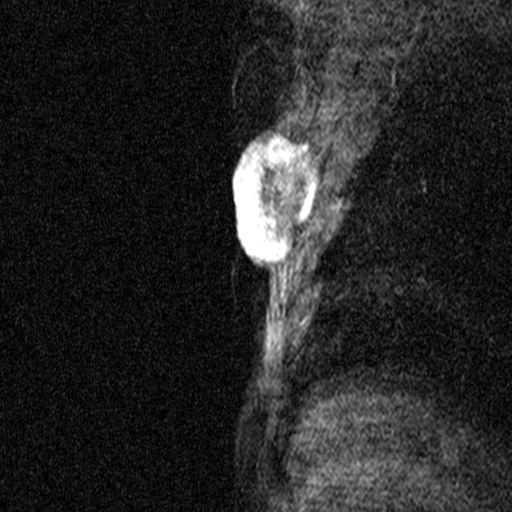
Breast MRI (dynamic contrast-enhanced), one sagittal slice. Slice 31 of 44 in the series (ordered by position). Dynamic contrast-enhanced study with each time point stored as its own series, time point 2 of 3 at this slice position (early post-contrast, ordered by acquisition time). 1.5 T. TE 4.5 ms, TR 11 ms. 3 mm slice thickness. 512 × 512 image matrix, field of view 200 × 200 mm. Female patient, age 44 years. From the clinical record (not read from this slice): setting: breast cancer imaged before/during neoadjuvant chemotherapy; receptor status: HR-positive, HER2-negative.
Annotated regions visible in this slice (semi-automatic segmentation, software-assisted and operator-edited):
- analysis volume of interest (the breast-tissue region the enhancement analysis was run in; not a lesion): bounding box <218,118,316,291> (left, top, right, bottom; pixels)
- tumour enhancement mask (voxels above the 90 % enhancement threshold inside the analysis volume of interest): <233,135,316,260>